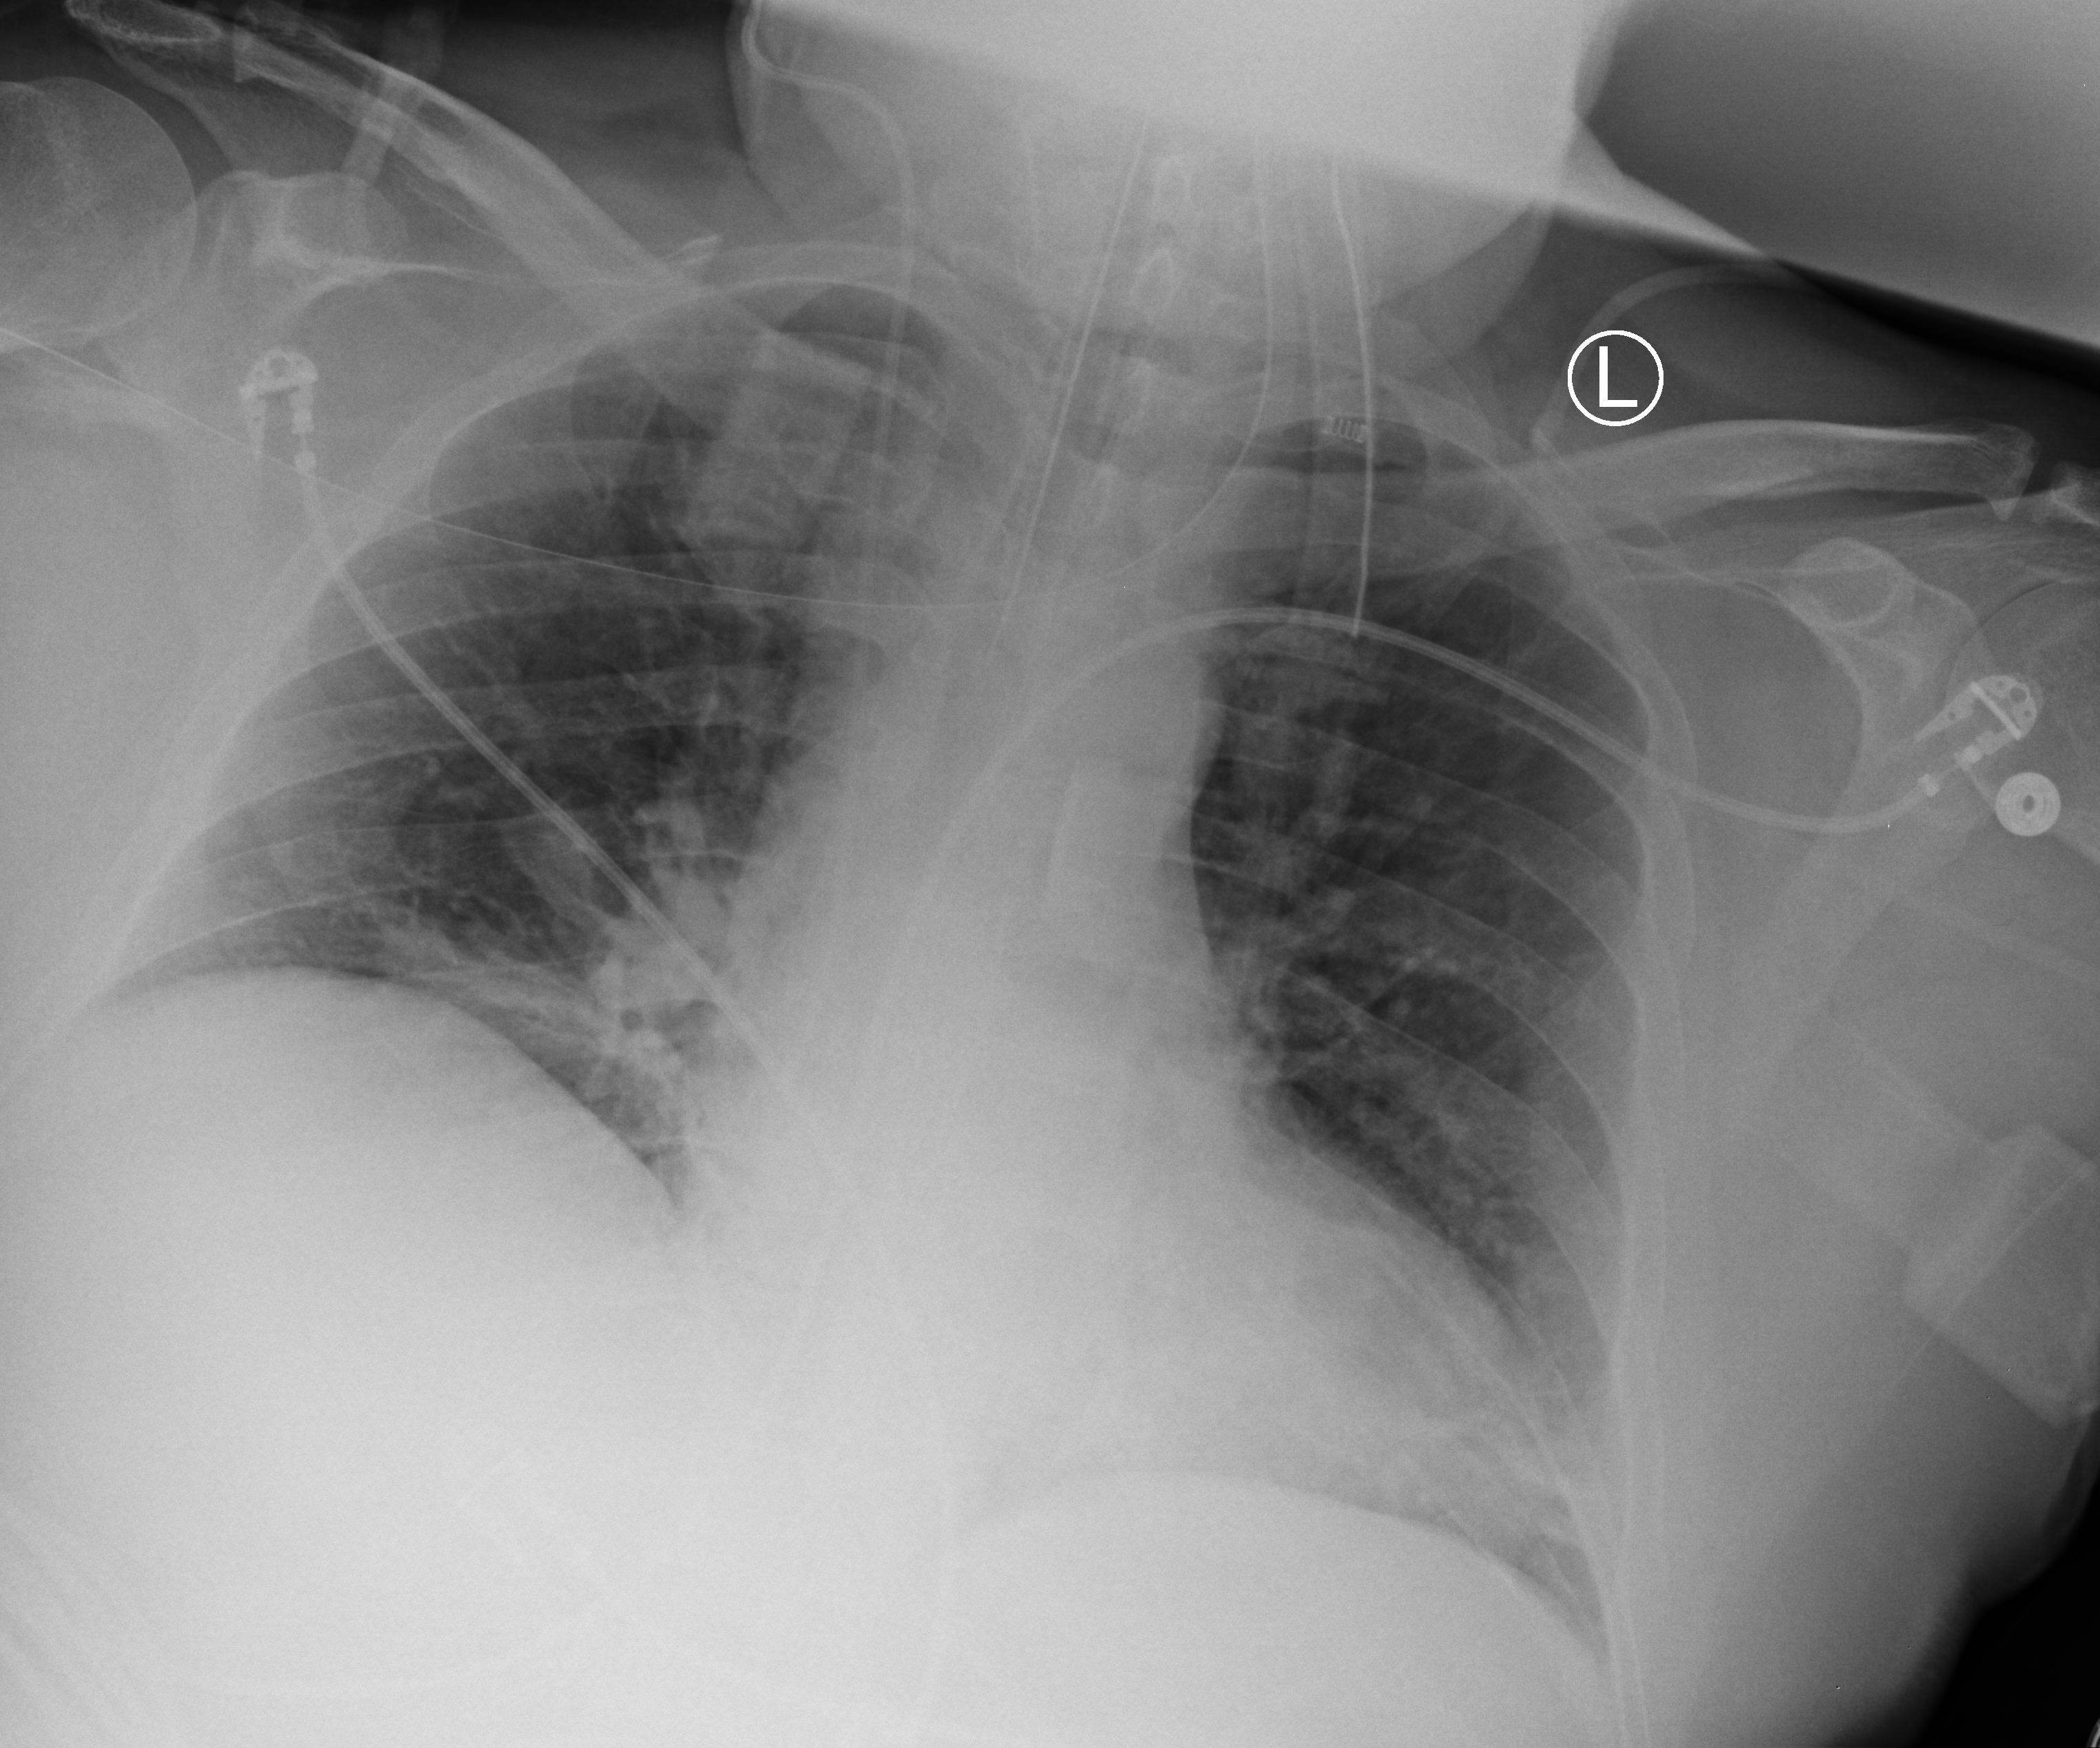
Chest X-ray (portable), anteroposterior (AP) projection. Male patient hospitalised with COVID-19, age 18–59 years.
Hospital-stay facts (about this admission, not read from this image; timing relative to this image not recorded):
- mechanically ventilated during this hospital stay: yes
- length of hospital stay: 17 days
- diabetes (admission record): yes